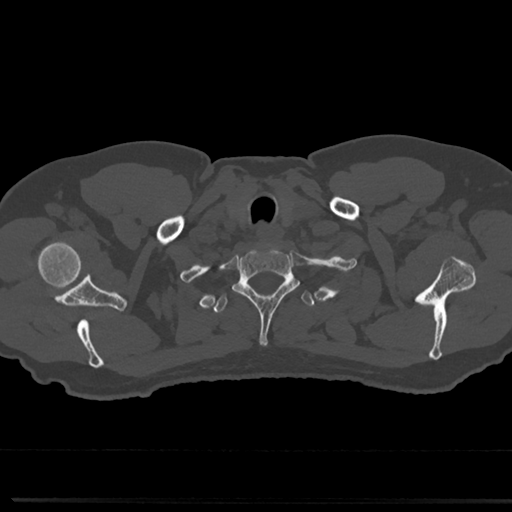
CT including the spine, one axial slice; position 667 of 817 along the scan axis; reconstruction kernel Br40s/3; bone window (W 1800 / L 400 HU); 0.5 mm slice thickness; 512 × 512 image matrix, field of view 355 × 355 mm. Male patient, age 61 years. From the clinical record (not read from this slice): primary cancer: prostate.
Annotated regions visible in this slice (semi-automatically segmented with operator editing):
- T1 vertebra: bounding box (x1, y1, x2, y2) in pixels: (233, 247, 298, 344)
- T2 vertebra: (212, 278, 315, 315)